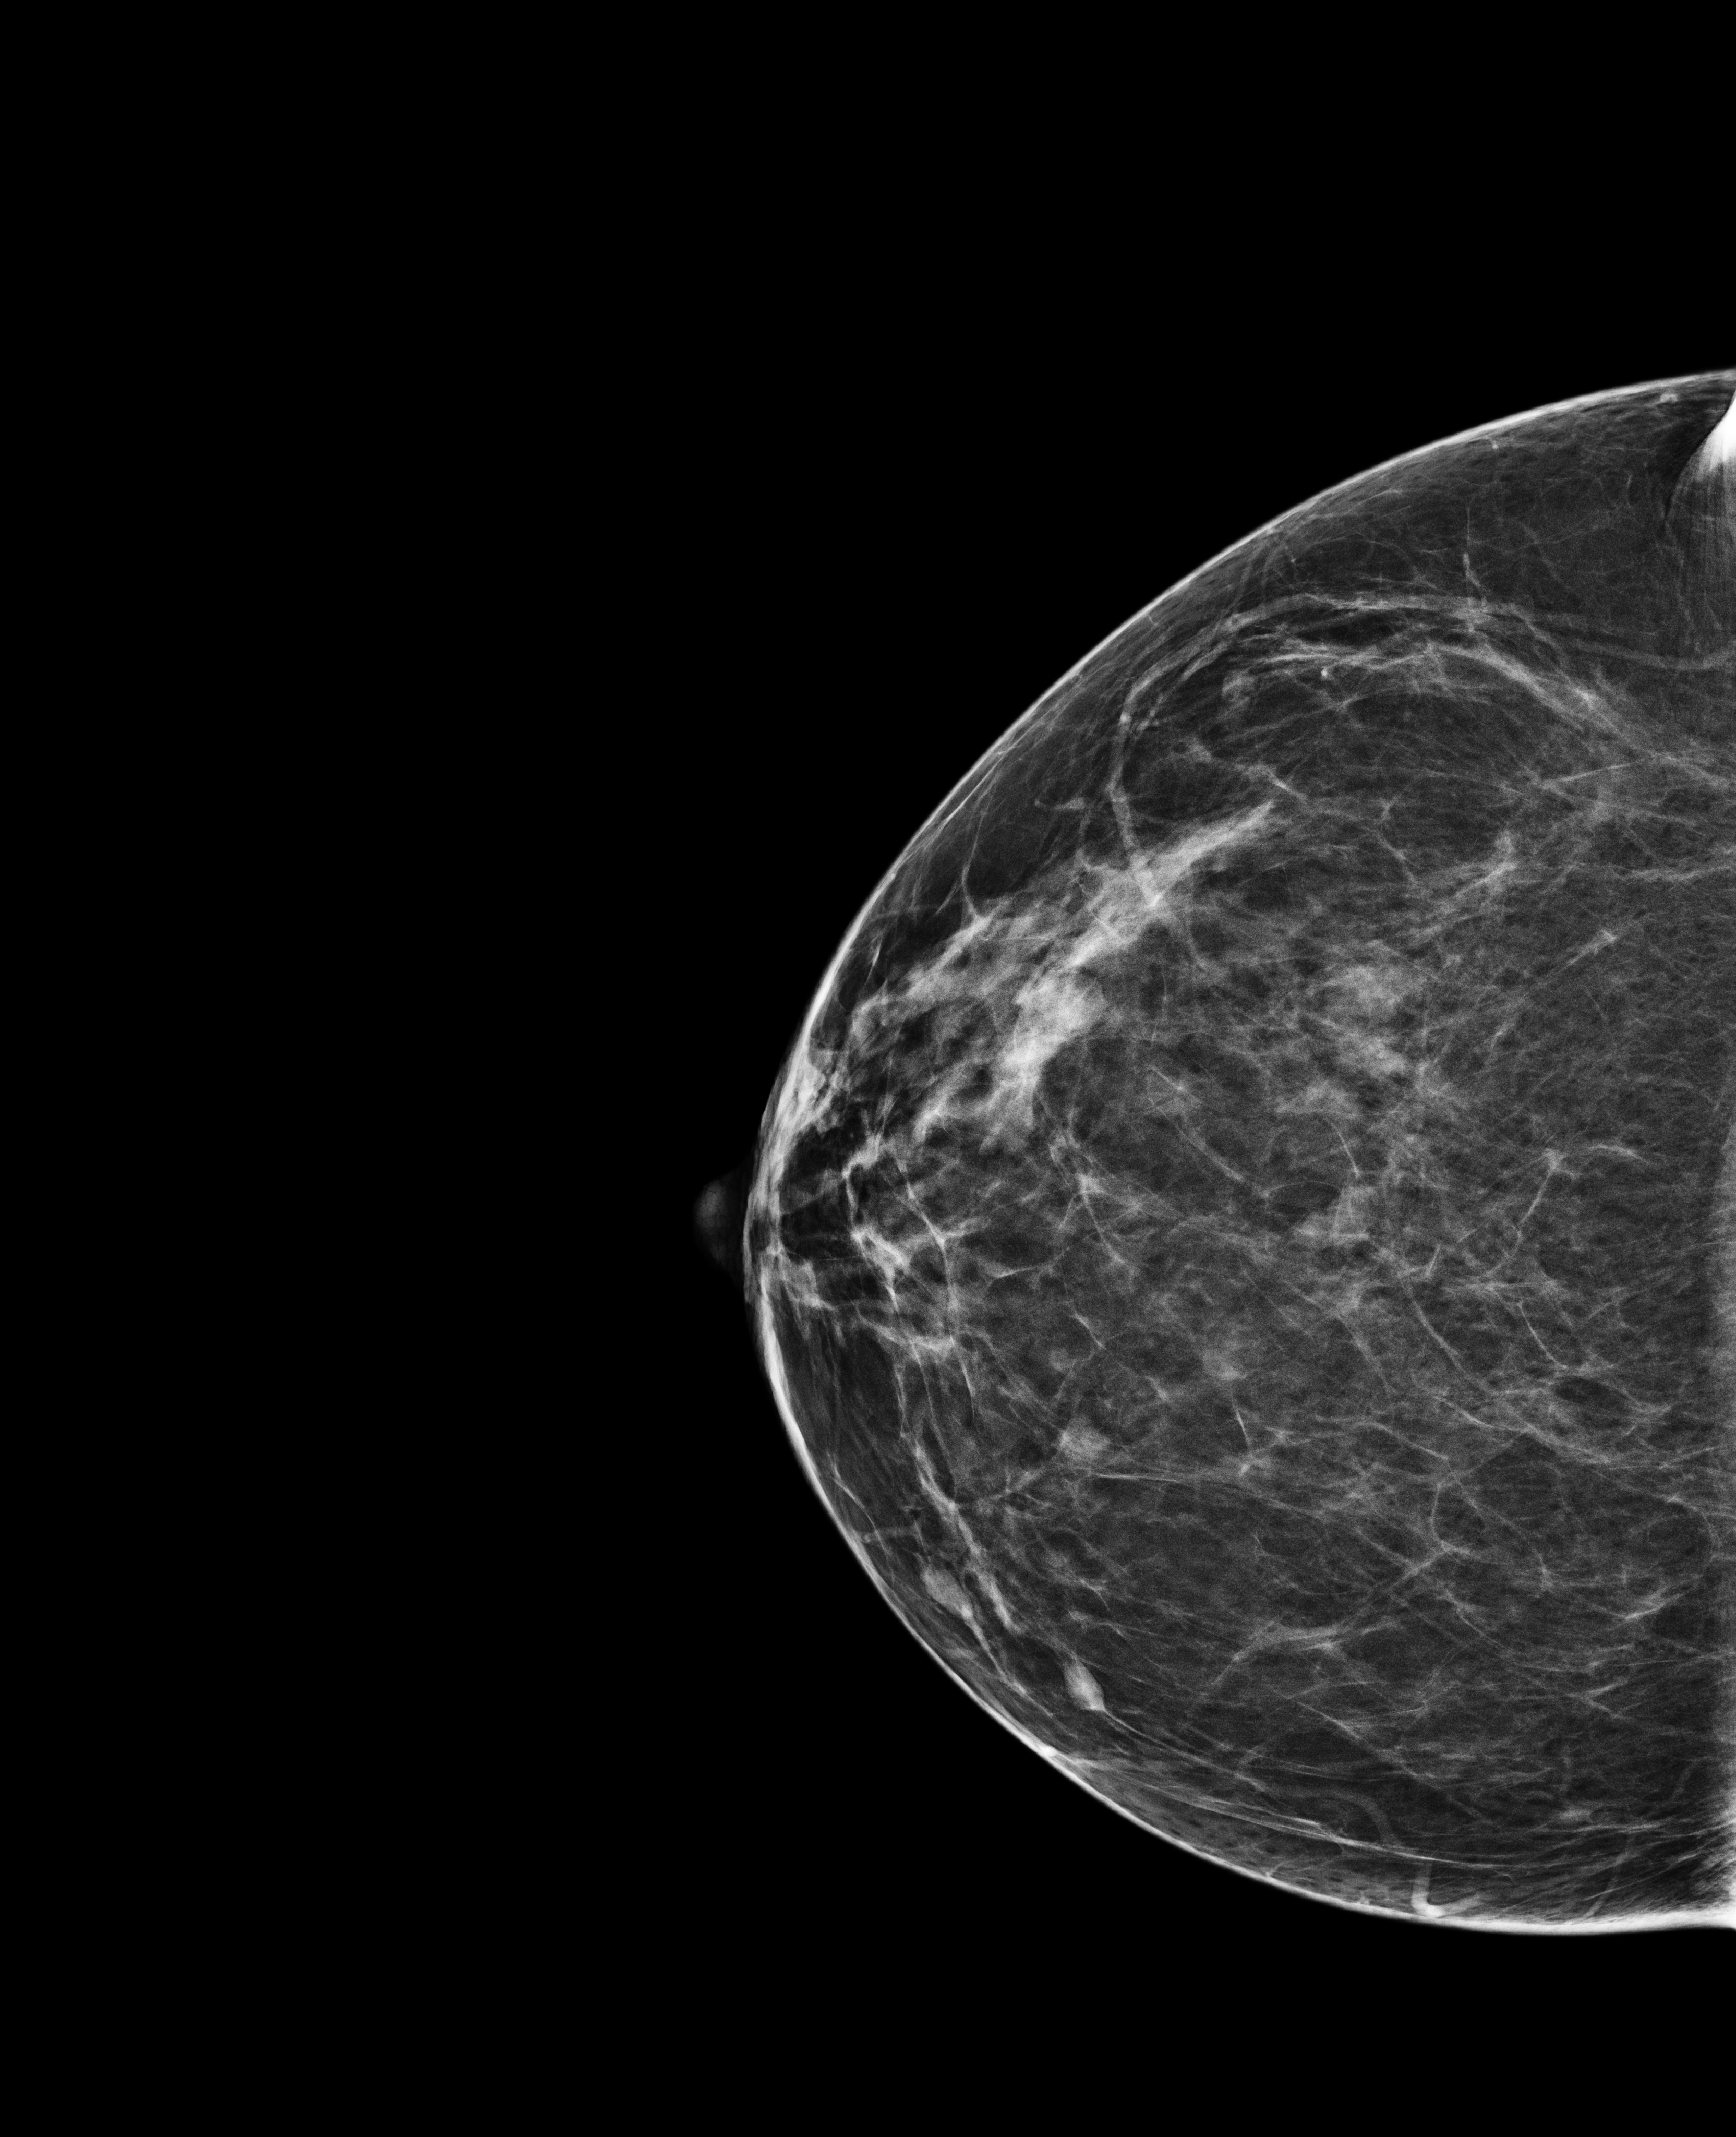
Digital mammogram (FFDM); right breast; craniocaudal (CC) view; screening examination; compressed breast thickness 58 mm. Female patient, age 64 years.
Breast density at the screening exam (both breasts): heterogeneously dense (BI-RADS density category c). Final BI-RADS assessment for this screening round (tomosynthesis exam, both breasts): category 2. Recall: no recall after this screen.